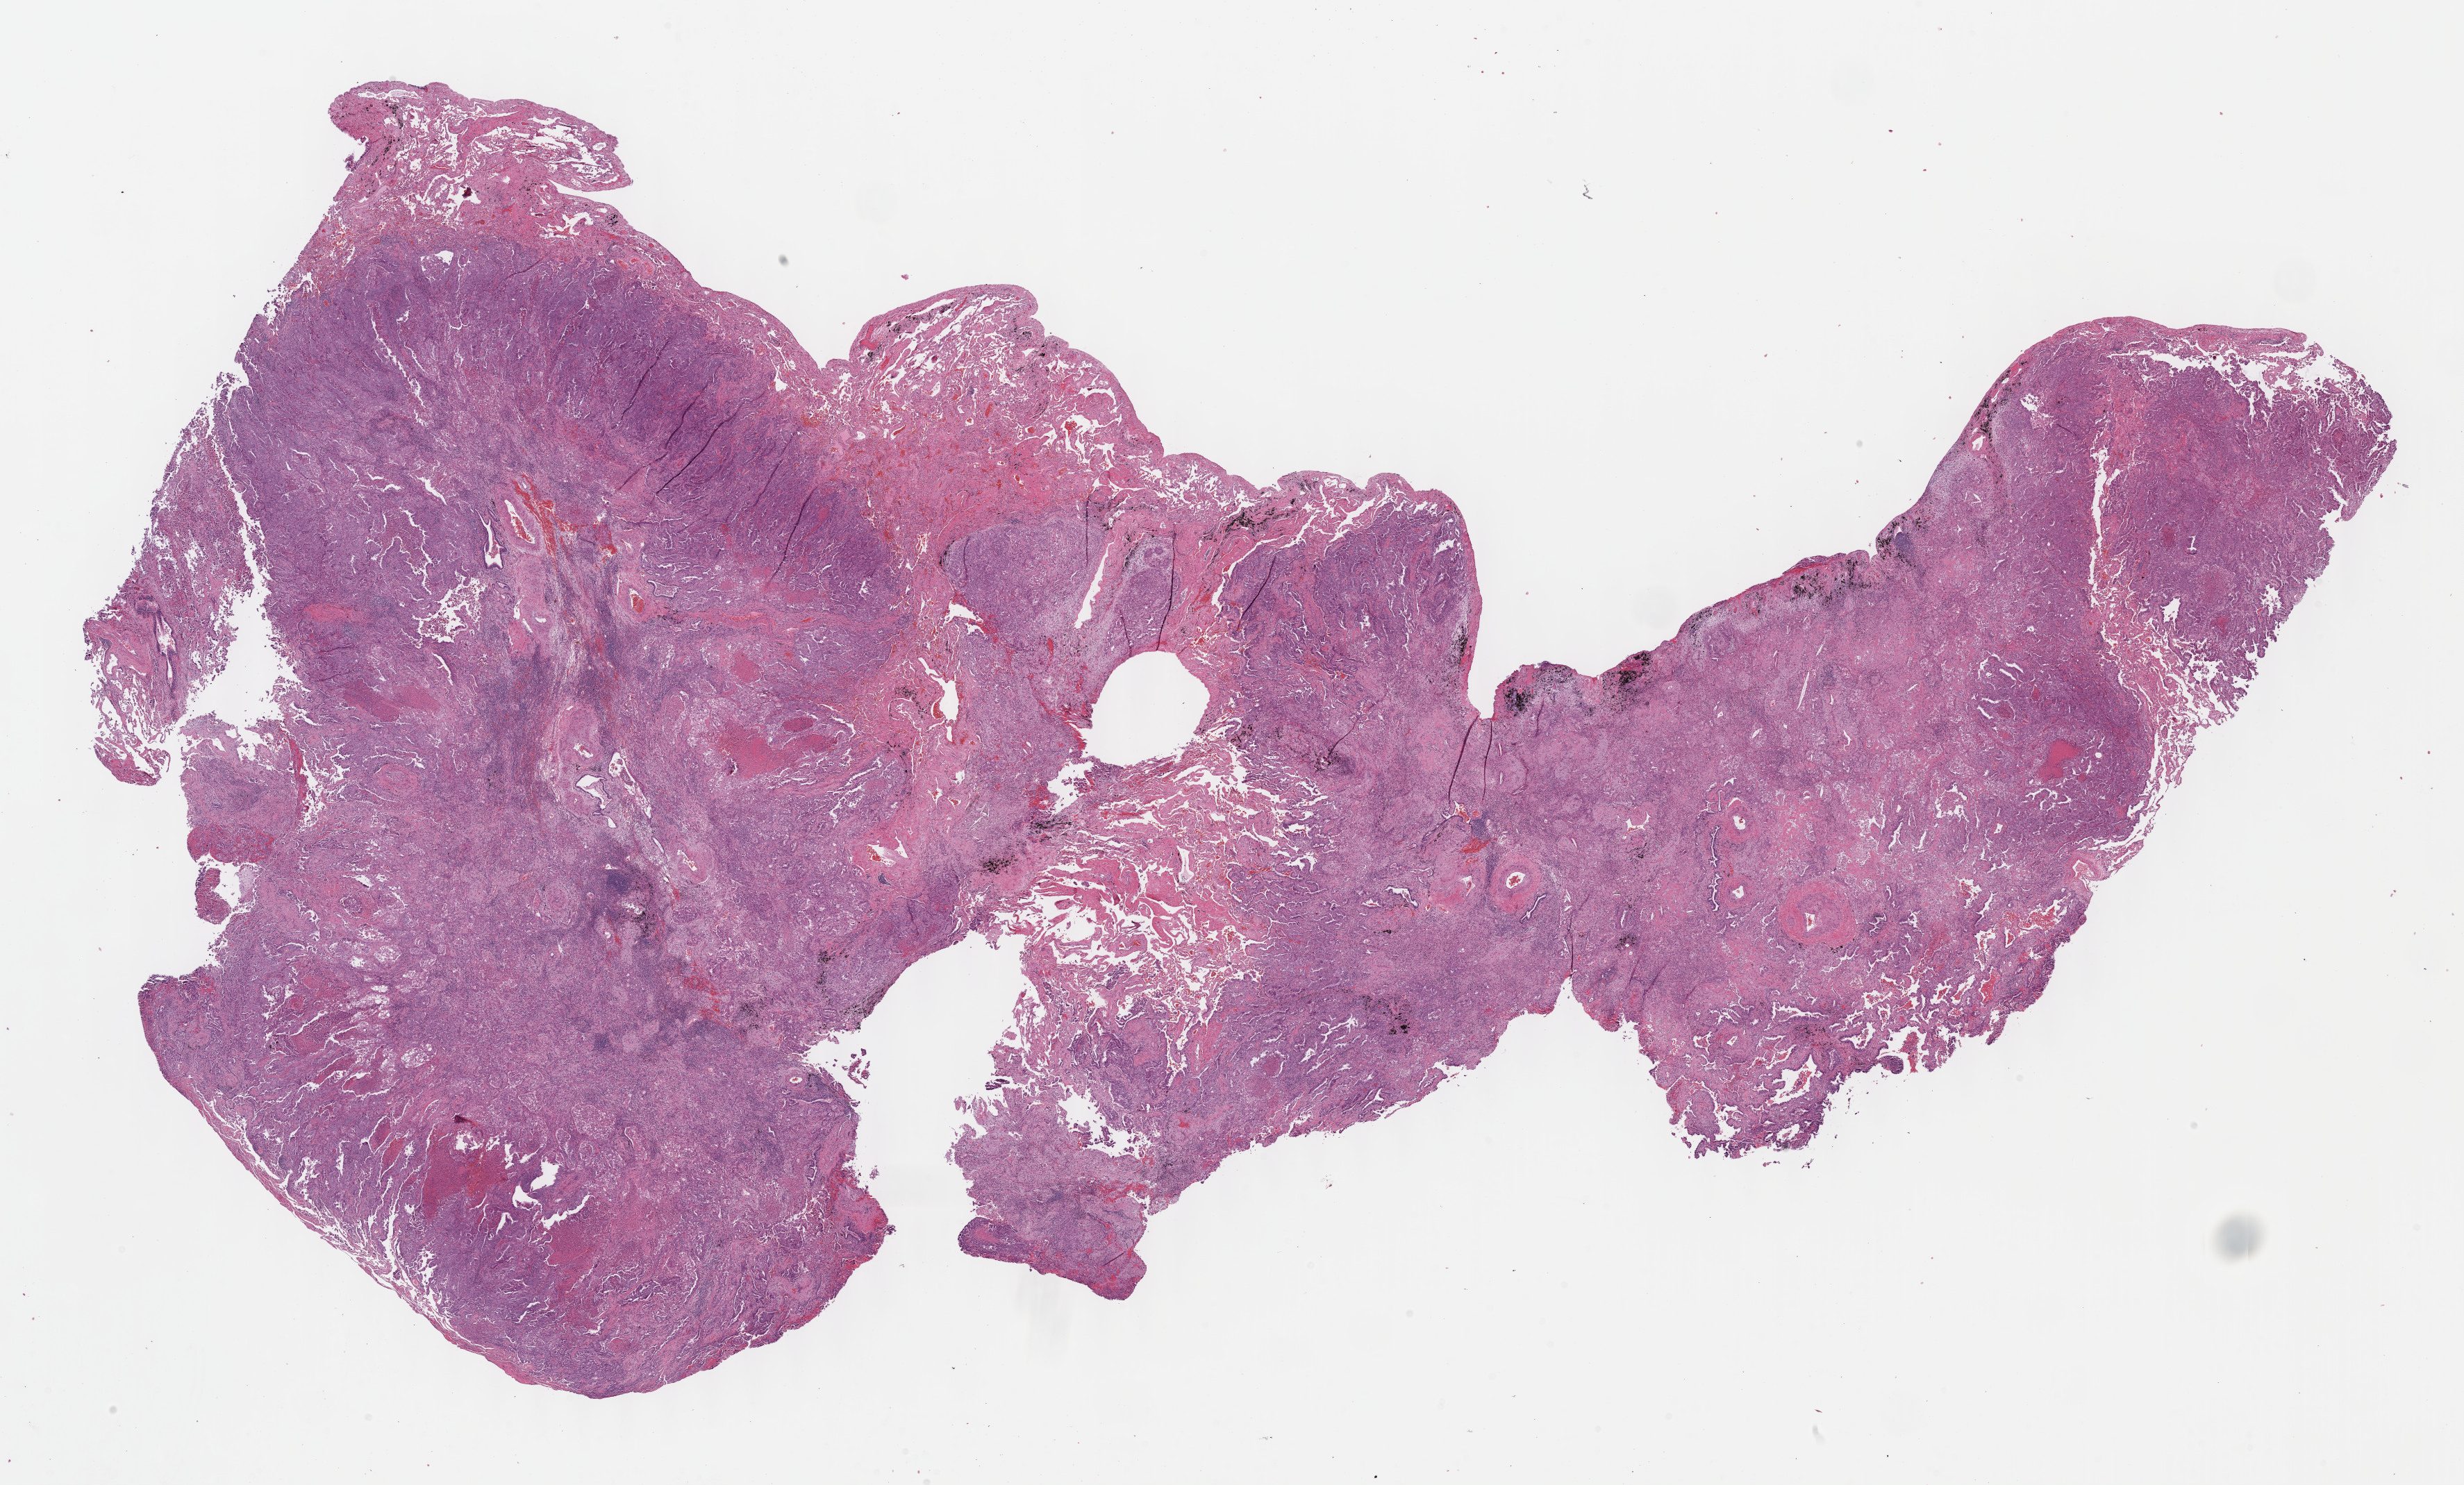
Digitized H&E-stained tissue section (whole slide), a low-resolution overview of the entire scanned area, about 28.7 x 17.3 mm (acquisition: 40x scan), FFPE section, primary tumour sample from the lung. Patient: male, age at initial diagnosis 61 years.
Laterality: right. Diagnosis: Adenocarcinoma, NOS (lower lobe, lung). AJCC pathologic stage: IIB (5th edition).